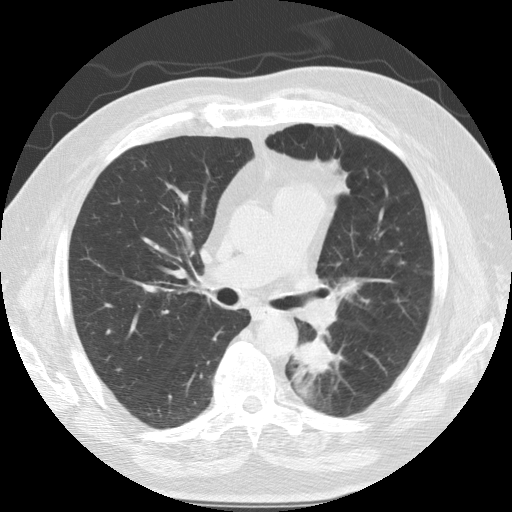
Low-dose screening chest CT, axial slice, baseline screening round, lung window (W 1500 / L -600 HU), standard (soft-tissue) reconstruction kernel (STANDARD), slice 54 of 124 in the series, 512 × 512 image matrix, field of view 360 × 360 mm. Male, age 68 years at enrolment. Former smoker at enrolment.
Expert-annotated lung lesion, box from (x=280, y=318) to (x=352, y=397) px. The screening reader recorded 3 non-calcified nodules or masses ≥4 mm on this exam (left lower lobe, lingula, right lower lobe); which of them this box marks is not recorded. Official screen result: positive, change unspecified: nodule(s) >= 4 mm or enlarging nodule(s), mass(es), or other non-specific abnormalities suspicious for lung cancer. Later outcome: lung cancer diagnosed 35 days after this screen — squamous cell carcinoma, NOS, left lower lobe, poorly differentiated (G3), stage IIB (AJCC 6th edition), 40 mm at pathology.